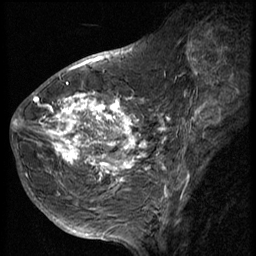
Breast MRI (dynamic contrast-enhanced), one sagittal slice; 3 images stored at this slice position (order not interpretable as contrast timing); 1.5 T; TE 4.2 ms, TR 9 ms; 2.5 mm slice thickness; 256 × 256 image matrix, field of view 180 × 180 mm. Female patient, age 49 years. From the clinical record (not read from this slice): setting: breast cancer imaged before/during neoadjuvant chemotherapy; receptor status: HER2-positive.
Structures marked on this image (semi-automatic segmentation, software-assisted and operator-edited):
- analysis volume of interest (the breast-tissue region the enhancement analysis was run in; not a lesion): bounding box <37,85,144,207> (left, top, right, bottom; pixels)
- tumour enhancement mask (voxels above the 140 % enhancement threshold inside the analysis volume of interest): <37,93,144,183>